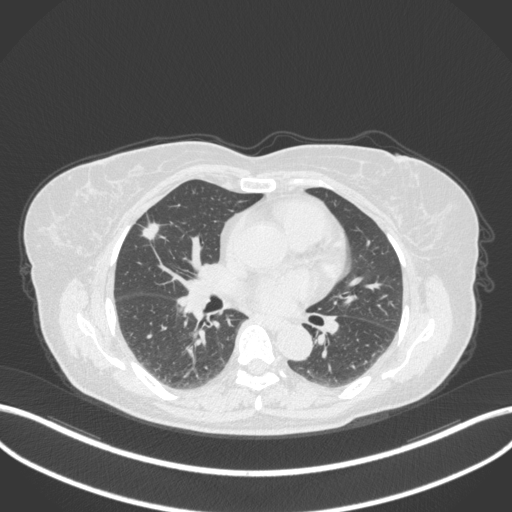
Chest CT, one axial slice; slice 175 of 310 in the series (ordered by position); lung window (W 1500 / L -600 HU); 1 mm slice thickness; 512 × 512 image matrix. Female patient, age 55 years. From the clinical record (not read from this slice): clinical TNM (as recorded): T1b N0 M0; histopathological grade: G2.
Structures marked on this image (bounding box drawn by a radiologist):
- lung tumour (recorded histology: adenocarcinoma): box from (x=137, y=215) to (x=162, y=244) px